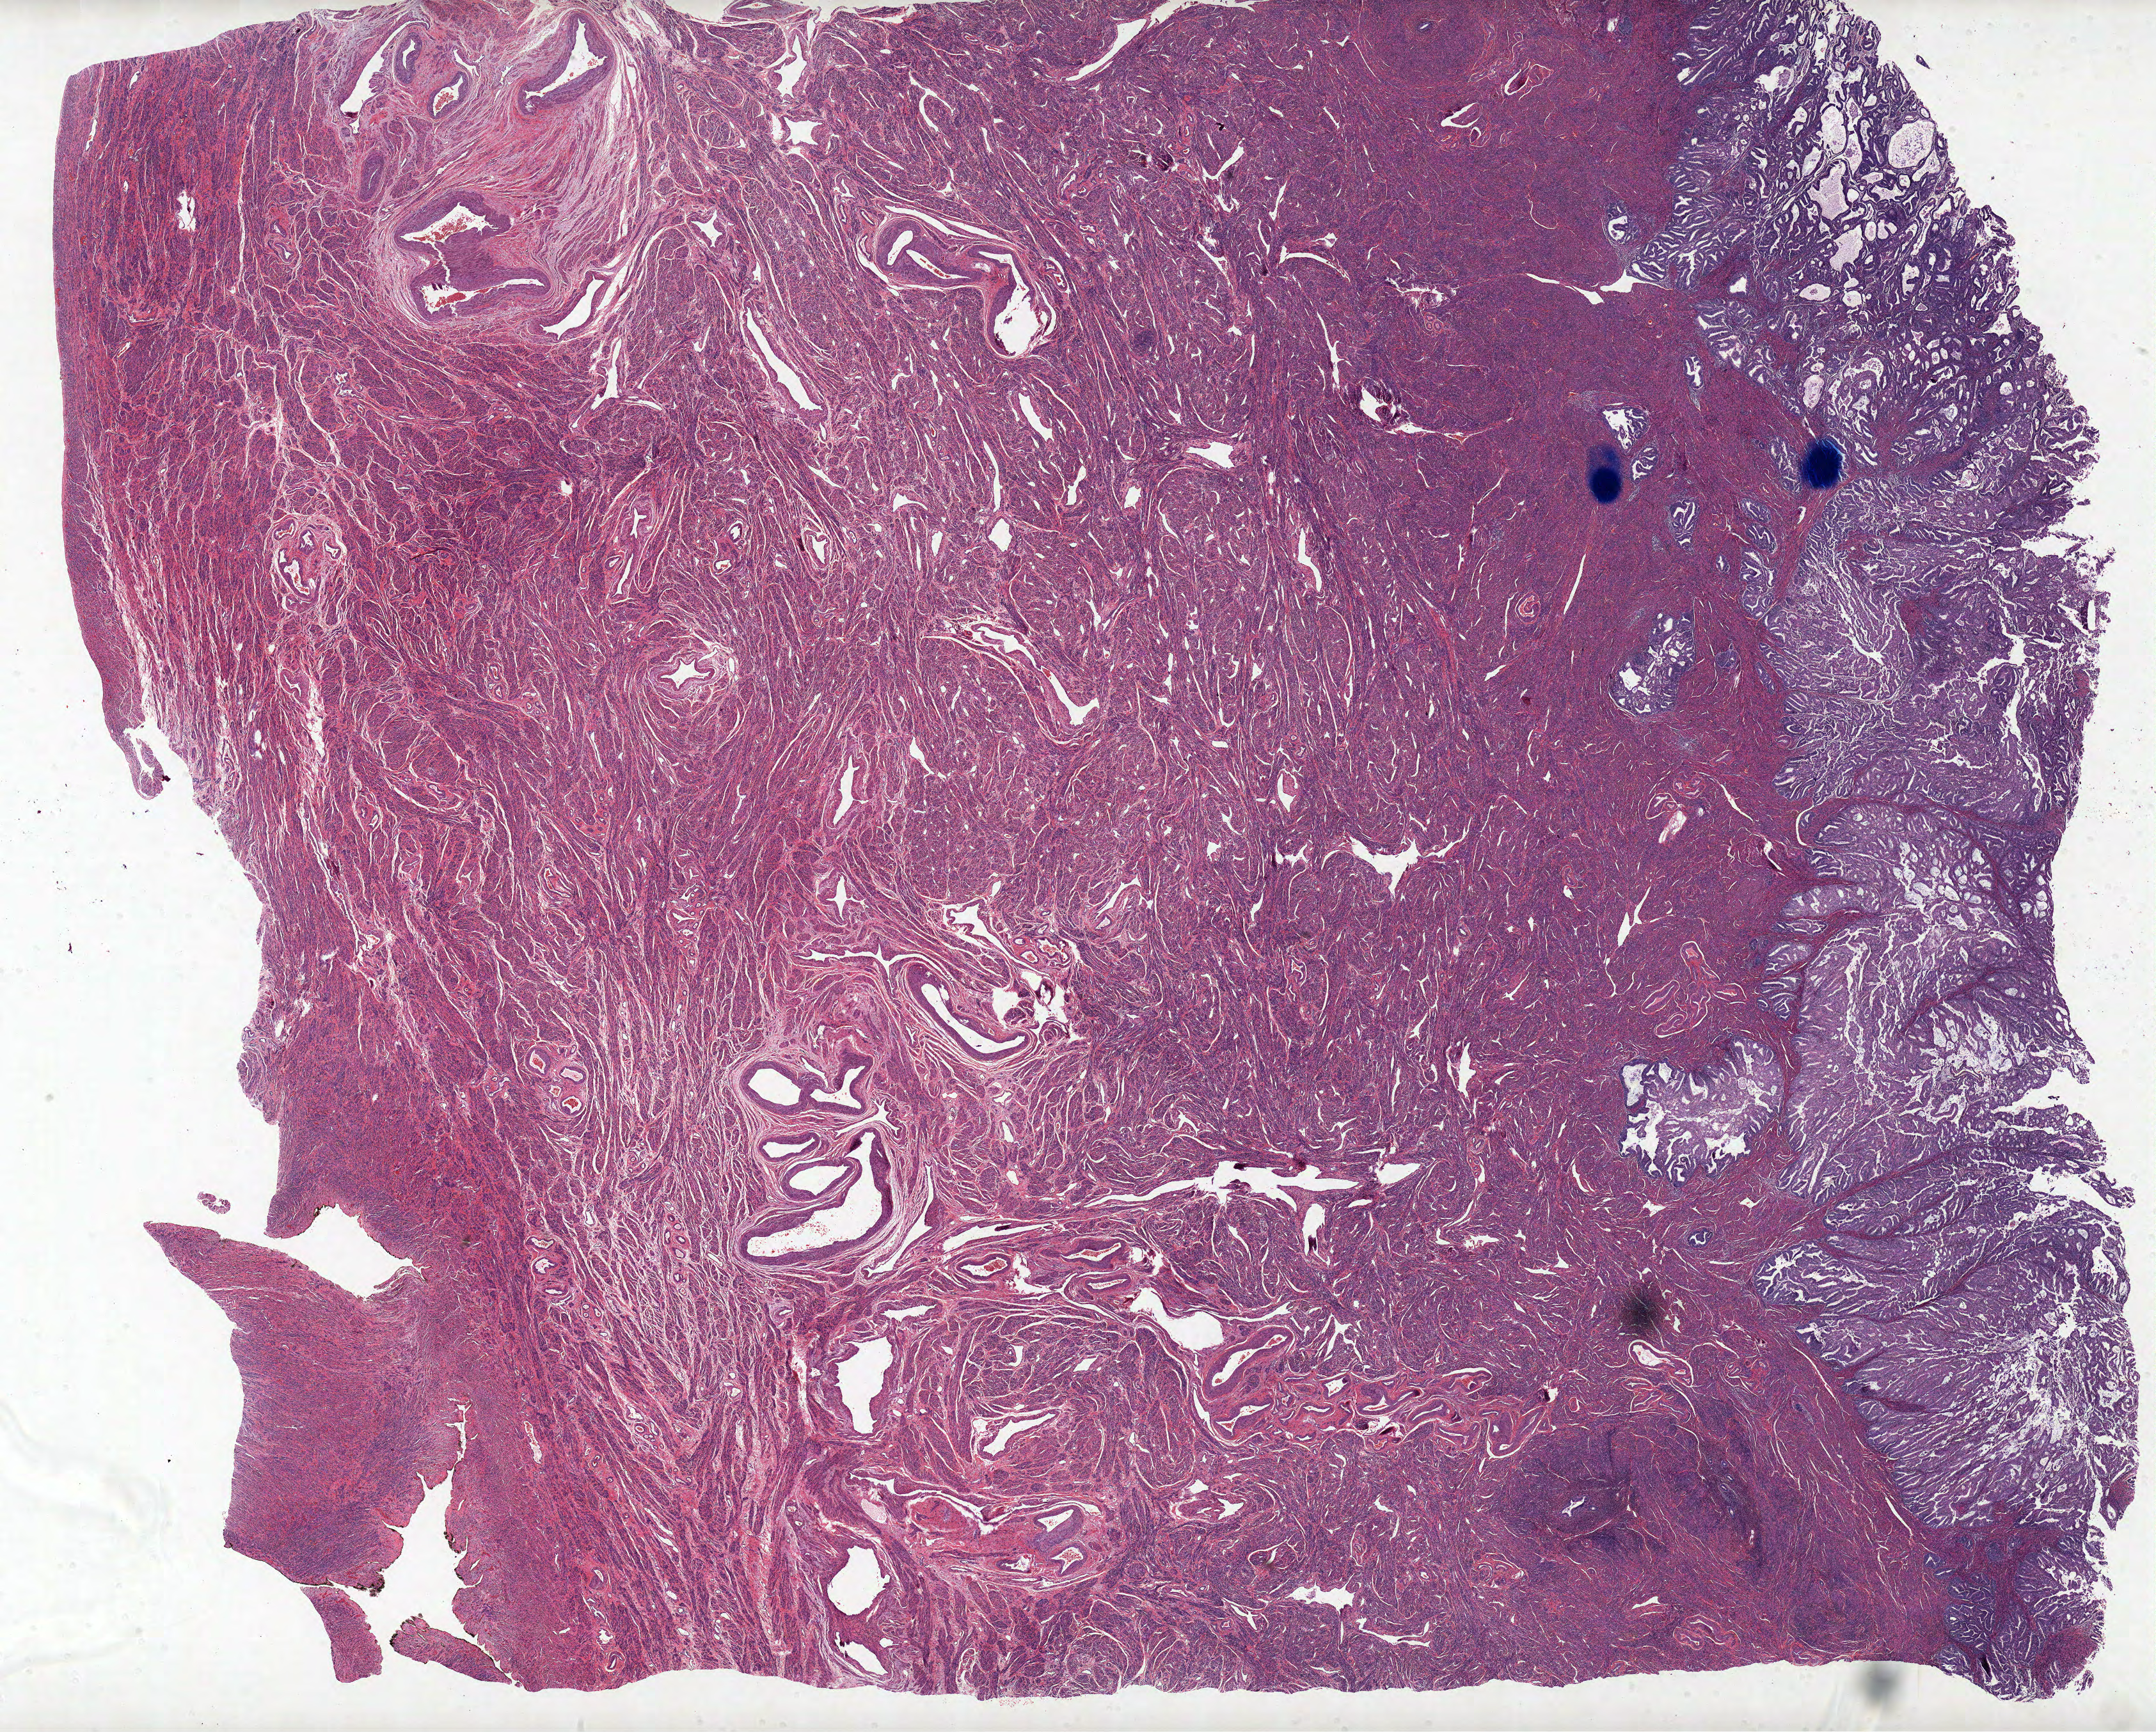
Hematoxylin and eosin (H&E) stained whole-slide image — shown as a low-resolution overview of the whole scanned area (about 26.9 x 21.6 mm, from a 20x scan). Formalin-fixed paraffin-embedded (FFPE) diagnostic section. Primary tumour sample from the uterus. Female, age 76 years at initial diagnosis. Histologic grade: G1 (well differentiated).
• FIGO stage: IA
• pathologic diagnosis: Endometrioid adenocarcinoma, NOS (endometrium)